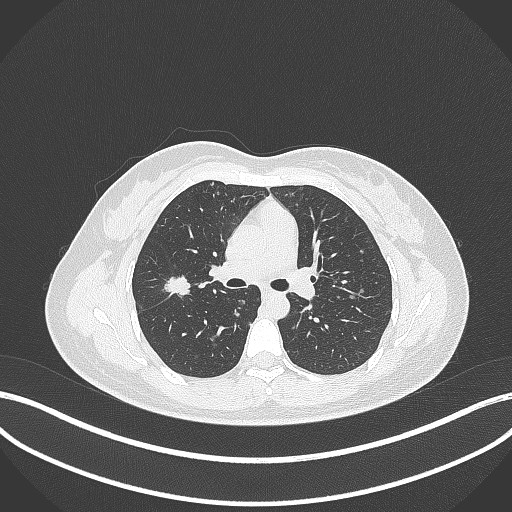
Chest CT, one axial slice; position 204 of 307 along the scan axis; 120 kVp; lung window (W 1500 / L -600 HU); 1 mm slice thickness; 512 × 512 image matrix, field of view 400 × 400 mm. Patient: female, 33 years. From the clinical record (not read from this slice): clinical TNM (as recorded): T1c N0 M0; histopathological grade: G2-G3.
Annotated regions visible in this slice (rectangle marked by the reading radiologist):
- lung tumour (recorded histology: adenocarcinoma): bounding box <162,272,194,299> (left, top, right, bottom; pixels)